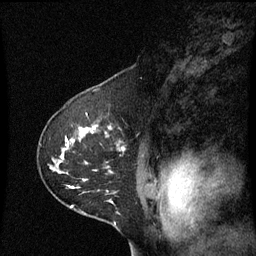
Breast MRI (dynamic contrast-enhanced), one sagittal slice; slice 44 of 60 in the series (ordered by position); dynamic contrast-enhanced series, image 2 of 3 at this slice position (ordered by acquisition); 1.5 T; TE 4.2 ms, TR 8.9 ms; 2 mm slice thickness; 256 × 256 image matrix, field of view 200 × 200 mm. Female patient, age 53 years. Case-level facts recorded for this patient, not image findings: setting: breast cancer imaged before/during neoadjuvant chemotherapy; receptor status: HR-positive, HER2-negative.
Structures marked on this image (semi-automatically segmented with operator editing):
- analysis volume of interest (the breast-tissue region the enhancement analysis was run in; not a lesion): bounding box [x1, y1, x2, y2] px = [38, 114, 145, 221]
- tumour enhancement mask (voxels above the 70 % enhancement threshold inside the analysis volume of interest): [66, 126, 125, 189]